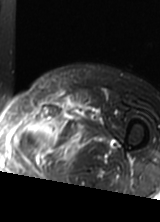
MRI of an extremity soft-tissue mass, one axial slice. Position 48 of 69 along the scan axis. T2-weighted fat-saturated. MR volume resampled by the dataset authors to the PET/CT grid (not the native acquisition matrix). 3.27 mm slice thickness. 160 × 222 image matrix, field of view 156 × 217 mm. Female patient. From the clinical record (not read from this slice): histological type: pleomorphic leiomyosarcoma; grade: high; site of the primary tumour: left thigh.
Structures marked on this image (expert contour drawn on MRI and transferred to this co-registered scan by the dataset authors):
- gross tumour volume including surrounding oedema: bounding box [x1, y1, x2, y2] px = [16, 95, 80, 162]